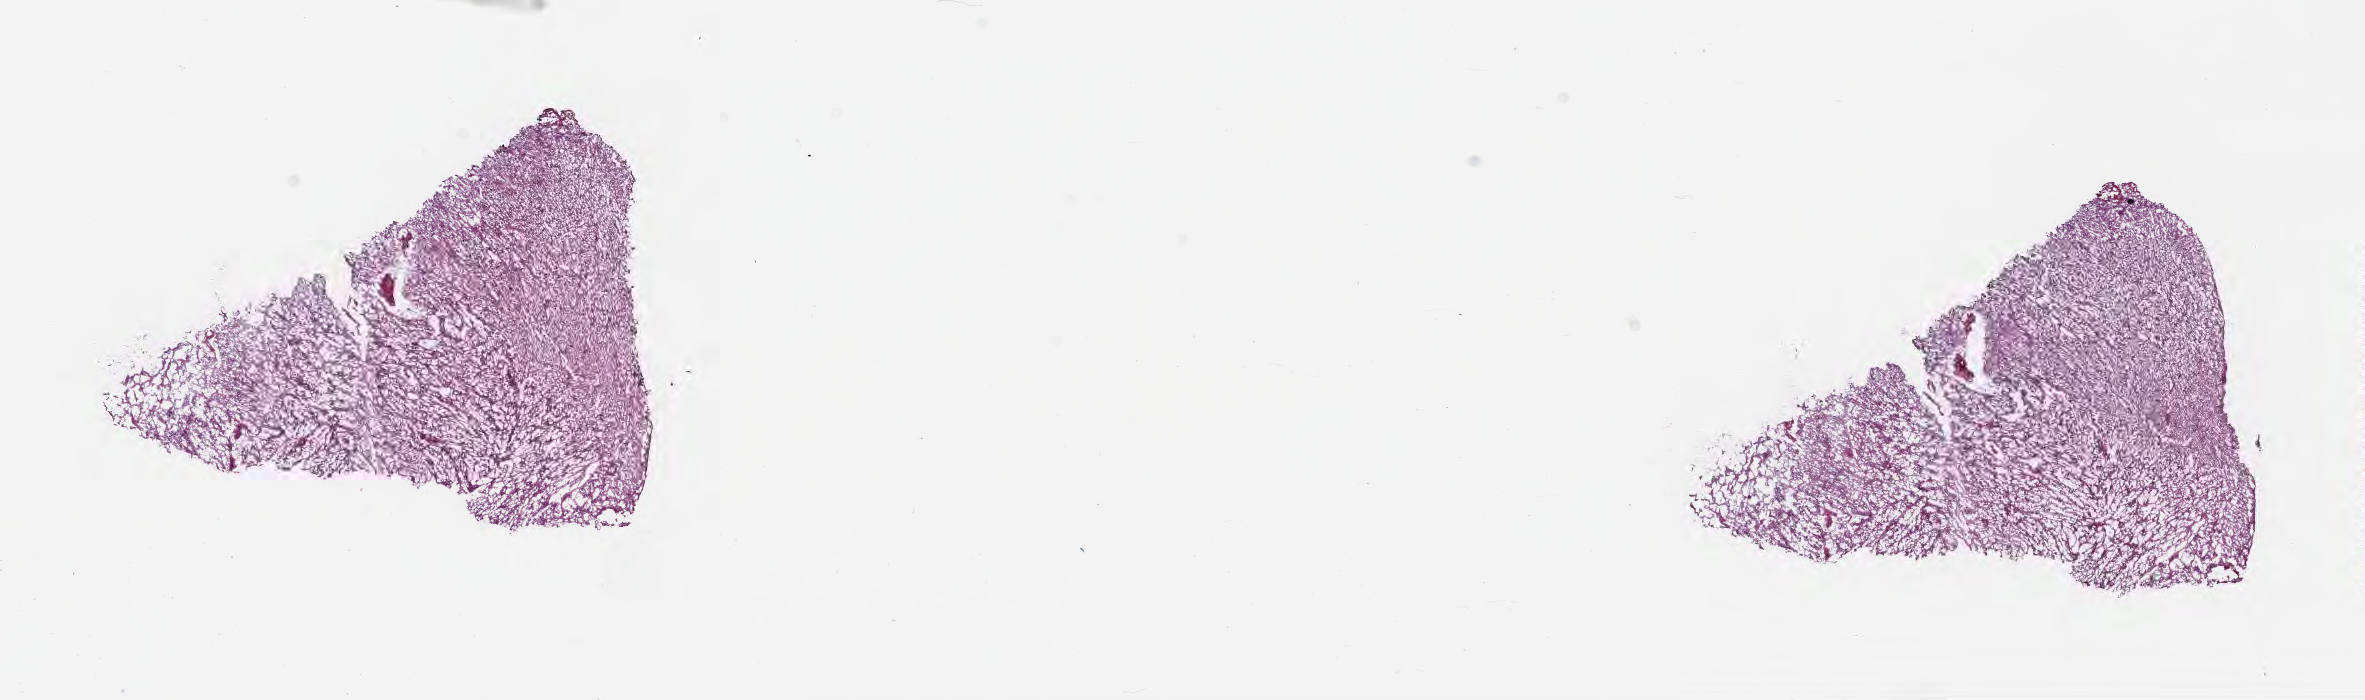
Whole-slide image, hematoxylin and eosin (H&E) stain — low-resolution overview of the scanned area, about 19.1 x 5.7 mm, frozen section, primary tumor, site: brain. Female patient; age at initial diagnosis 63 years. Pathologist review of this section (percent, as recorded): tumor cells 84%, tumor nuclei 91%, stromal cells 8%, necrosis 0%, normal cells 8%. Inflammatory infiltration, as recorded: lymphocyte infiltration 0%, monocyte infiltration 0%, neutrophil infiltration 0%.
• section: bottom of the tissue portion
• diagnosis: Glioblastoma, NOS